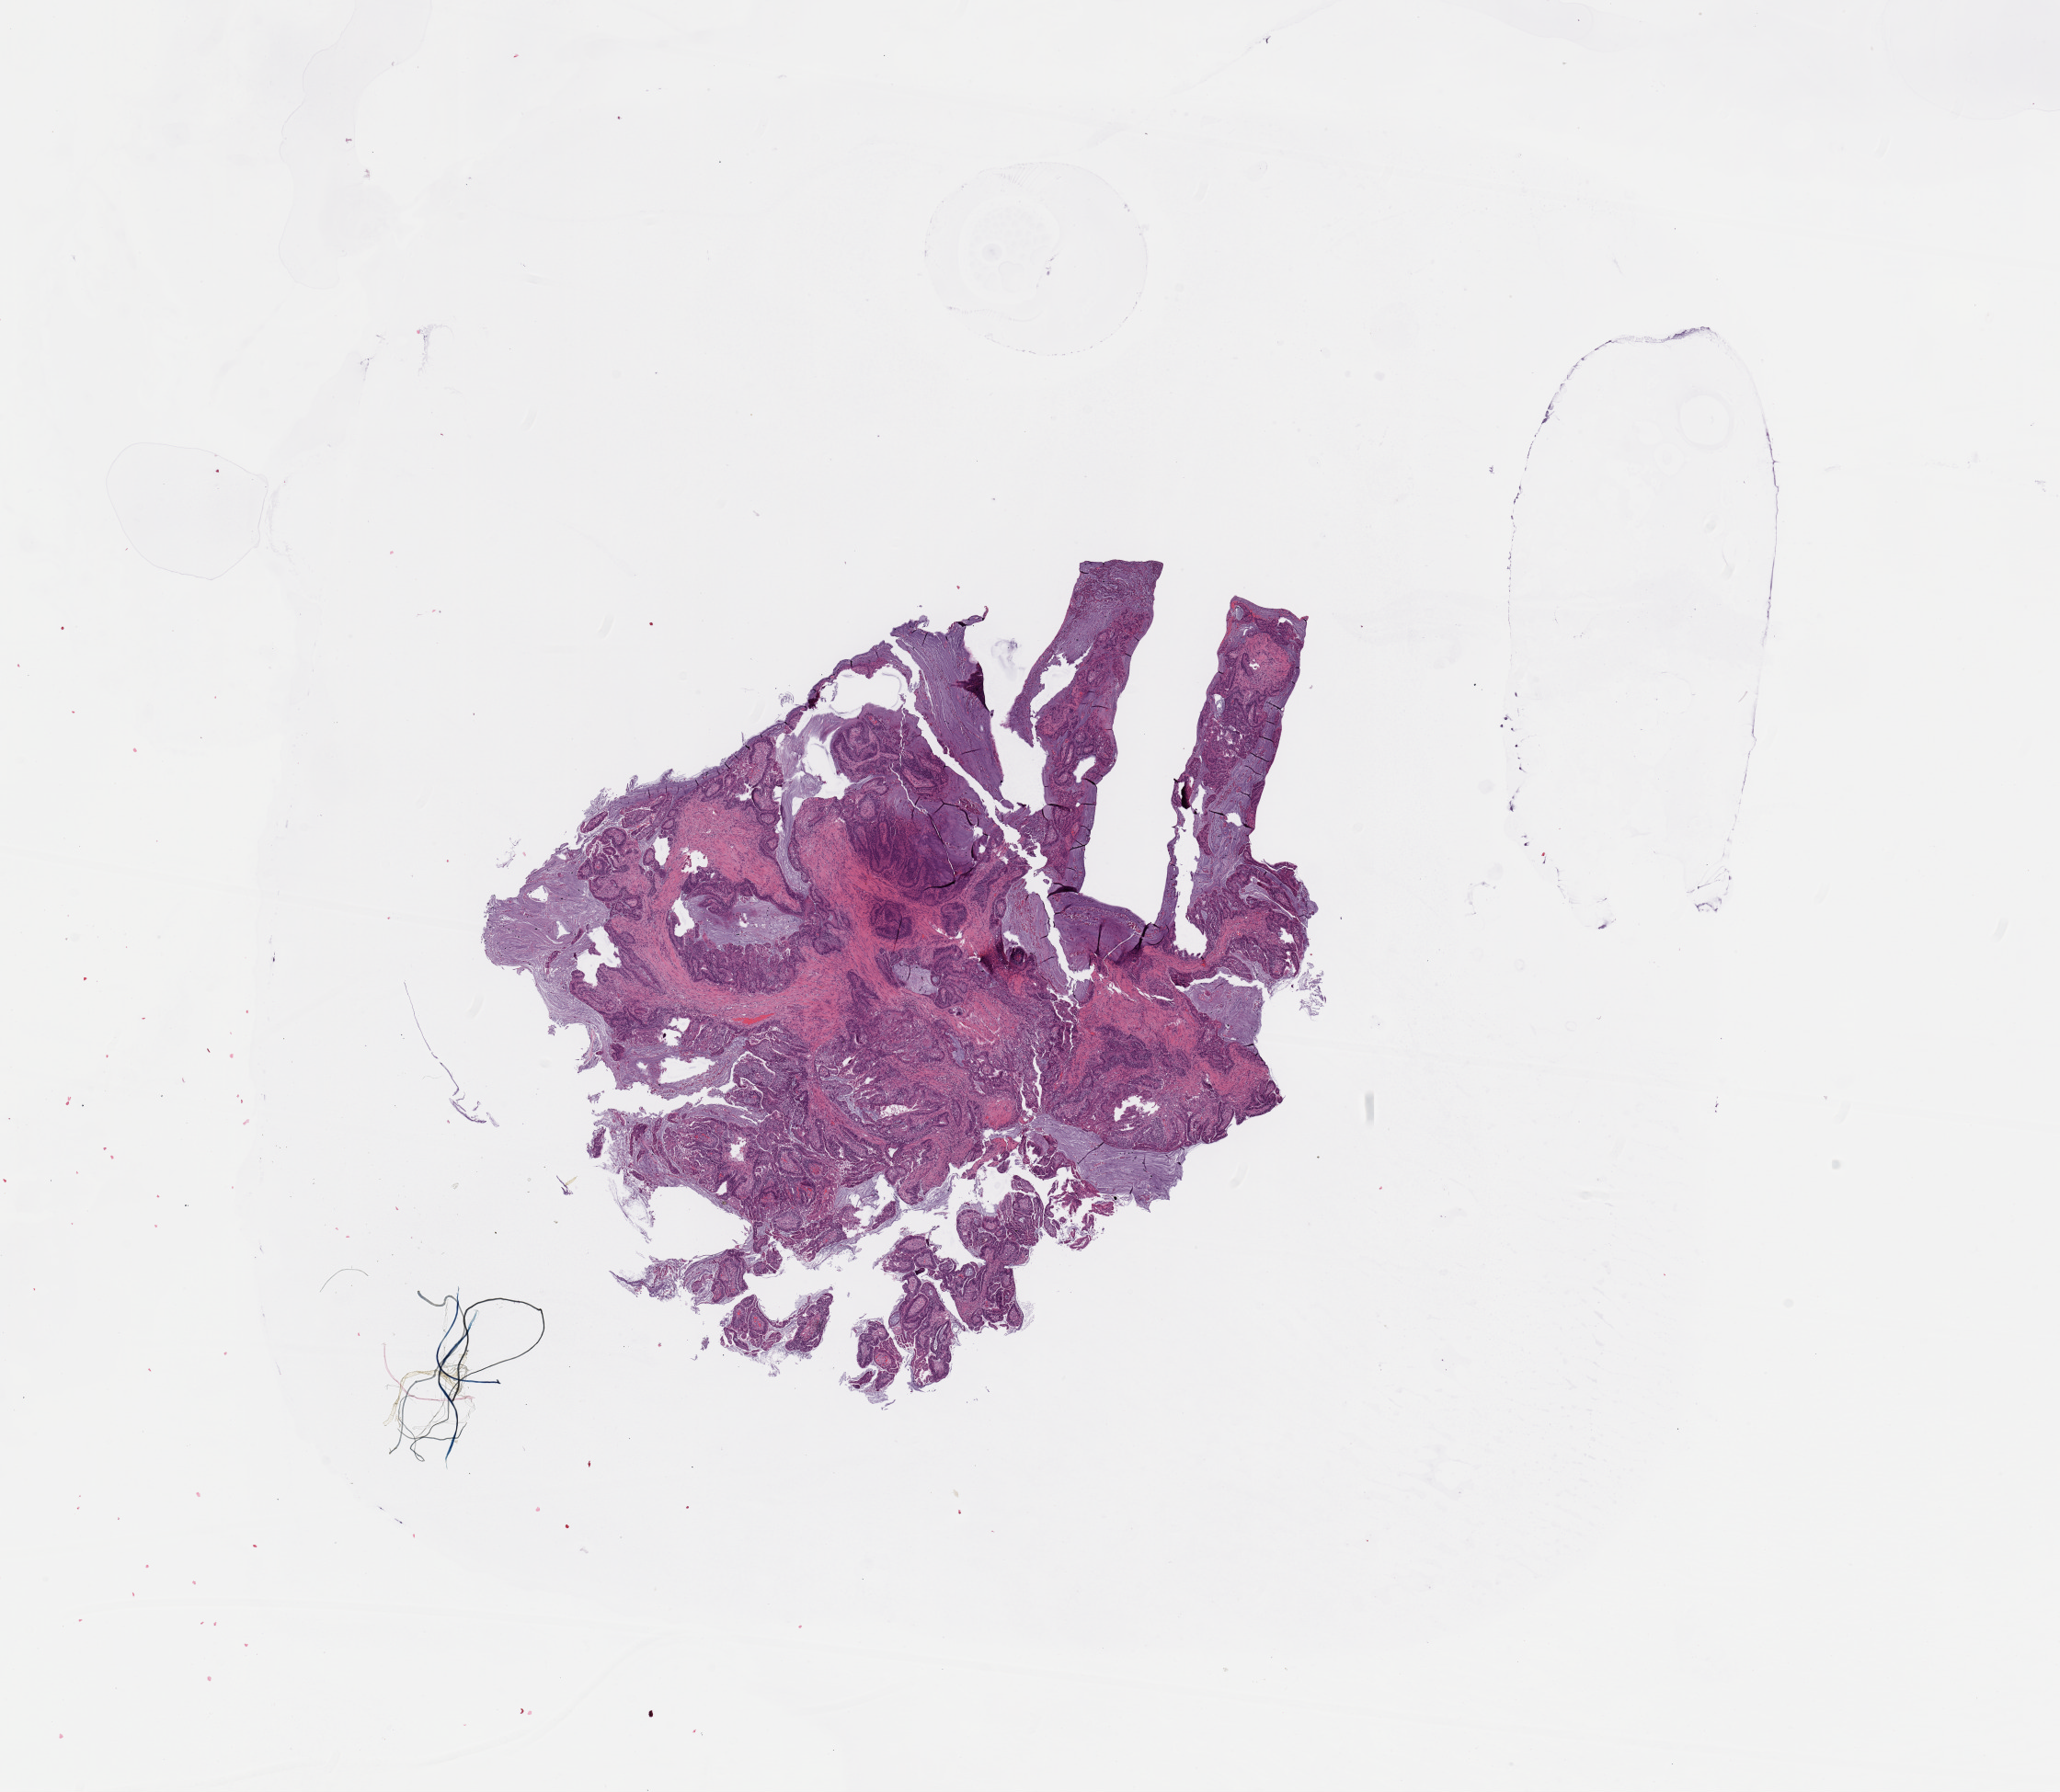
Whole-slide histology image, H&E-stained — whole scanned area (about 17.7 x 15.4 mm, acquisition: 20x scan) shown as a low-resolution overview. Tumour tissue sample, uterus. Patient: female, age 46 years. Histologic grade: G2 (moderately differentiated).
AJCC pathologic stage: I. Histologic diagnosis: Endometrioid adenocarcinoma, NOS.